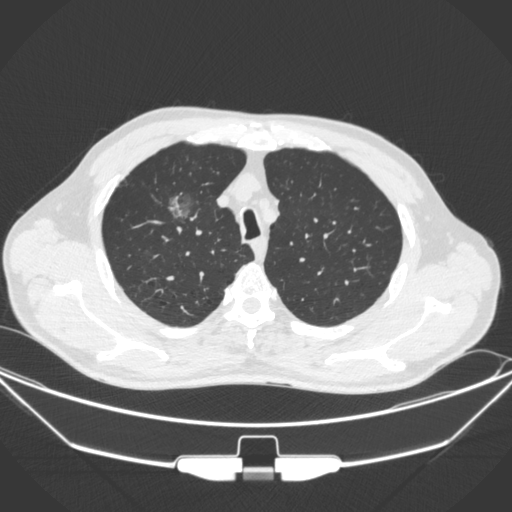
Chest CT, one axial slice; position 273 of 355 along the scan axis; lung window (W 1500 / L -600 HU); 512 × 512 image matrix, field of view 399 × 399 mm. Patient: male, 67 years. Case-level facts recorded for this patient, not image findings: clinical TNM (as recorded): T1c N0 M0; histopathological grade: G2.
Outlined on this slice (bounding box drawn by a radiologist):
- lung tumour (recorded histology: adenocarcinoma): bounding box <164,184,202,224> (left, top, right, bottom; pixels)